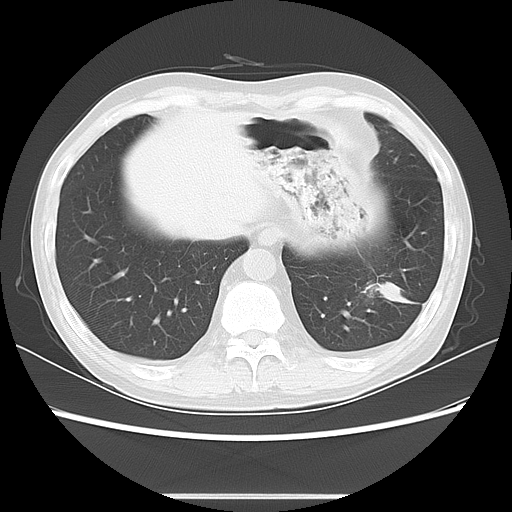
Chest CT, one axial slice. Position 20 of 63 along the scan axis. Lung window (W 1500 / L -600 HU). 5 mm slice thickness. 512 × 512 image matrix, field of view 347 × 347 mm. Patient: male, 49 years. From the clinical record (not read from this slice): clinical TNM (as recorded): T3 N0 M0; histopathological grade: G2-3.
Structures marked on this image (bounding box drawn by a radiologist):
- lung tumour (recorded histology: squamous cell carcinoma): bounding box <371,273,415,310> (left, top, right, bottom; pixels)